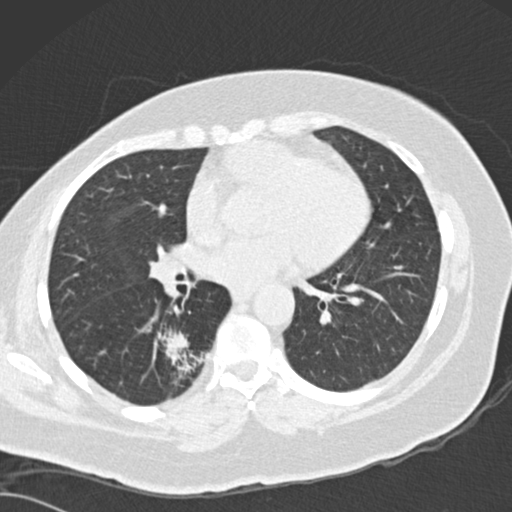
Low-dose screening chest CT, axial slice. First (baseline) screen. Lung window (W 1500 / L -600 HU). Female, age 66 years at enrolment.
Expert reader's lesion annotation, bounding box (x1, y1, x2, y2) in pixels: (153, 324, 223, 395). The screening reader recorded 3 non-calcified nodules or masses ≥4 mm on this exam; which of them this box marks is not recorded. Official screen result: positive, change unspecified: nodule(s) >= 4 mm or enlarging nodule(s), mass(es), or other non-specific abnormalities suspicious for lung cancer. Later outcome: lung cancer diagnosed 67 days after this screen — adenocarcinoma, NOS, right lower lobe, well differentiated (G1), stage IB (AJCC 6th edition), 55 mm at pathology.